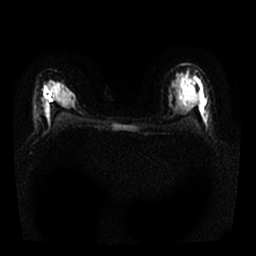
Breast MRI, one axial slice. Diffusion-weighted series; image 2 of 4 stored at this slice position (different b-values; order by instance number). 1.5 T. 4 mm slice thickness. 256 × 256 image matrix, field of view 320 × 320 mm. Female patient.
Outlined on this slice (manually delineated by an expert):
- tumour on diffusion-weighted imaging: bounding box (x1, y1, x2, y2) in pixels: (44, 86, 53, 97)